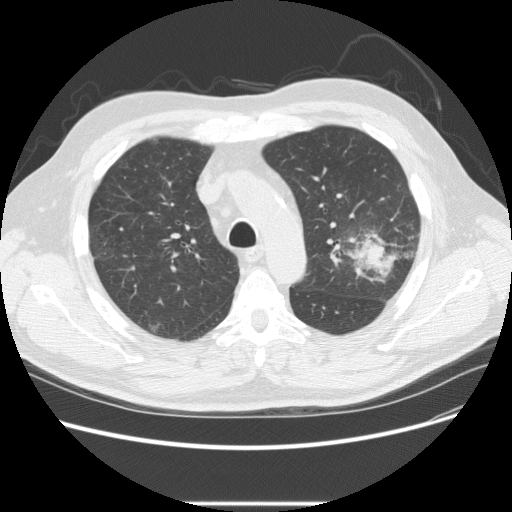
Low-dose screening chest CT, axial slice, baseline annual screen, lung window (W 1500 / L -600 HU), standard (soft-tissue) reconstruction kernel (STANDARD), slice 68 of 233 in the series. Male participant, aged 73 years at enrolment. Former smoker at enrolment.
Expert reader's lesion annotation, bounding box (x1, y1, x2, y2) in pixels: (332, 215, 419, 287). The screening reader recorded 2 non-calcified nodules or masses ≥4 mm on this exam (left upper lobe, right upper lobe); which of them this box marks is not recorded. Official screen result: positive, change unspecified: nodule(s) >= 4 mm or enlarging nodule(s), mass(es), or other non-specific abnormalities suspicious for lung cancer.